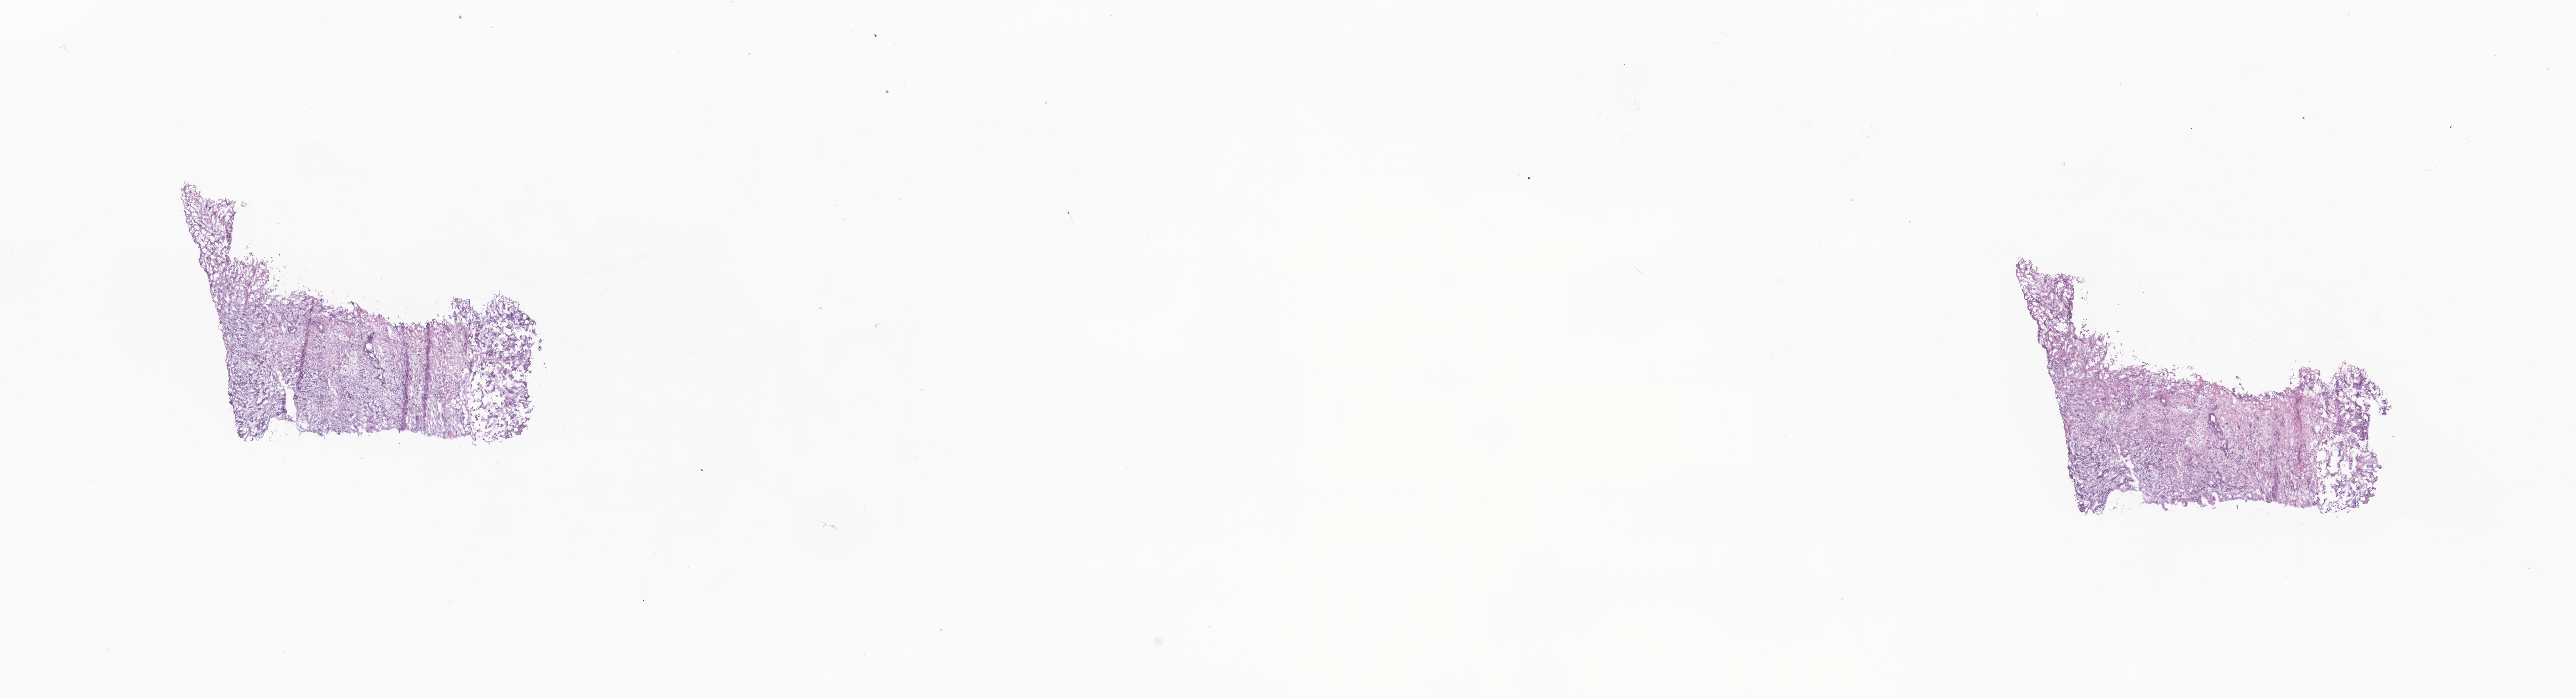
Digitized H&E-stained section — shown as a low-resolution overview of the whole scanned area (about 26.1 x 7.1 mm); frozen section; specimen: primary tumor; site: breast (right). Female, age 58 years at initial diagnosis. Composition of this section per pathologist review: tumor cells 100%, tumor nuclei 55%, stromal cells 0%, necrosis 0%, normal cells 0%. Inflammatory infiltration, as recorded: lymphocyte infiltration 0%, monocyte infiltration 0%, neutrophil infiltration 0%.
Diagnosis: Infiltrating duct carcinoma, NOS.